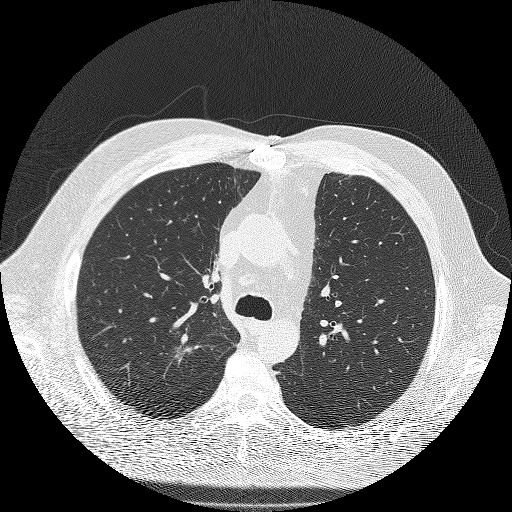
Low-dose screening chest CT, one axial slice. Slice 137 of 180 in the series (ordered by position). Reconstruction kernel FC51. 120 kVp. Lung window (W 1500 / L -600 HU). 2 mm slice thickness. 512 × 512 image matrix.
Structures marked on this image (outlined manually by an expert reader):
- lesion 1 (tumor, upper lobe of right lung): bounding box [x1, y1, x2, y2] px = [175, 333, 199, 364]